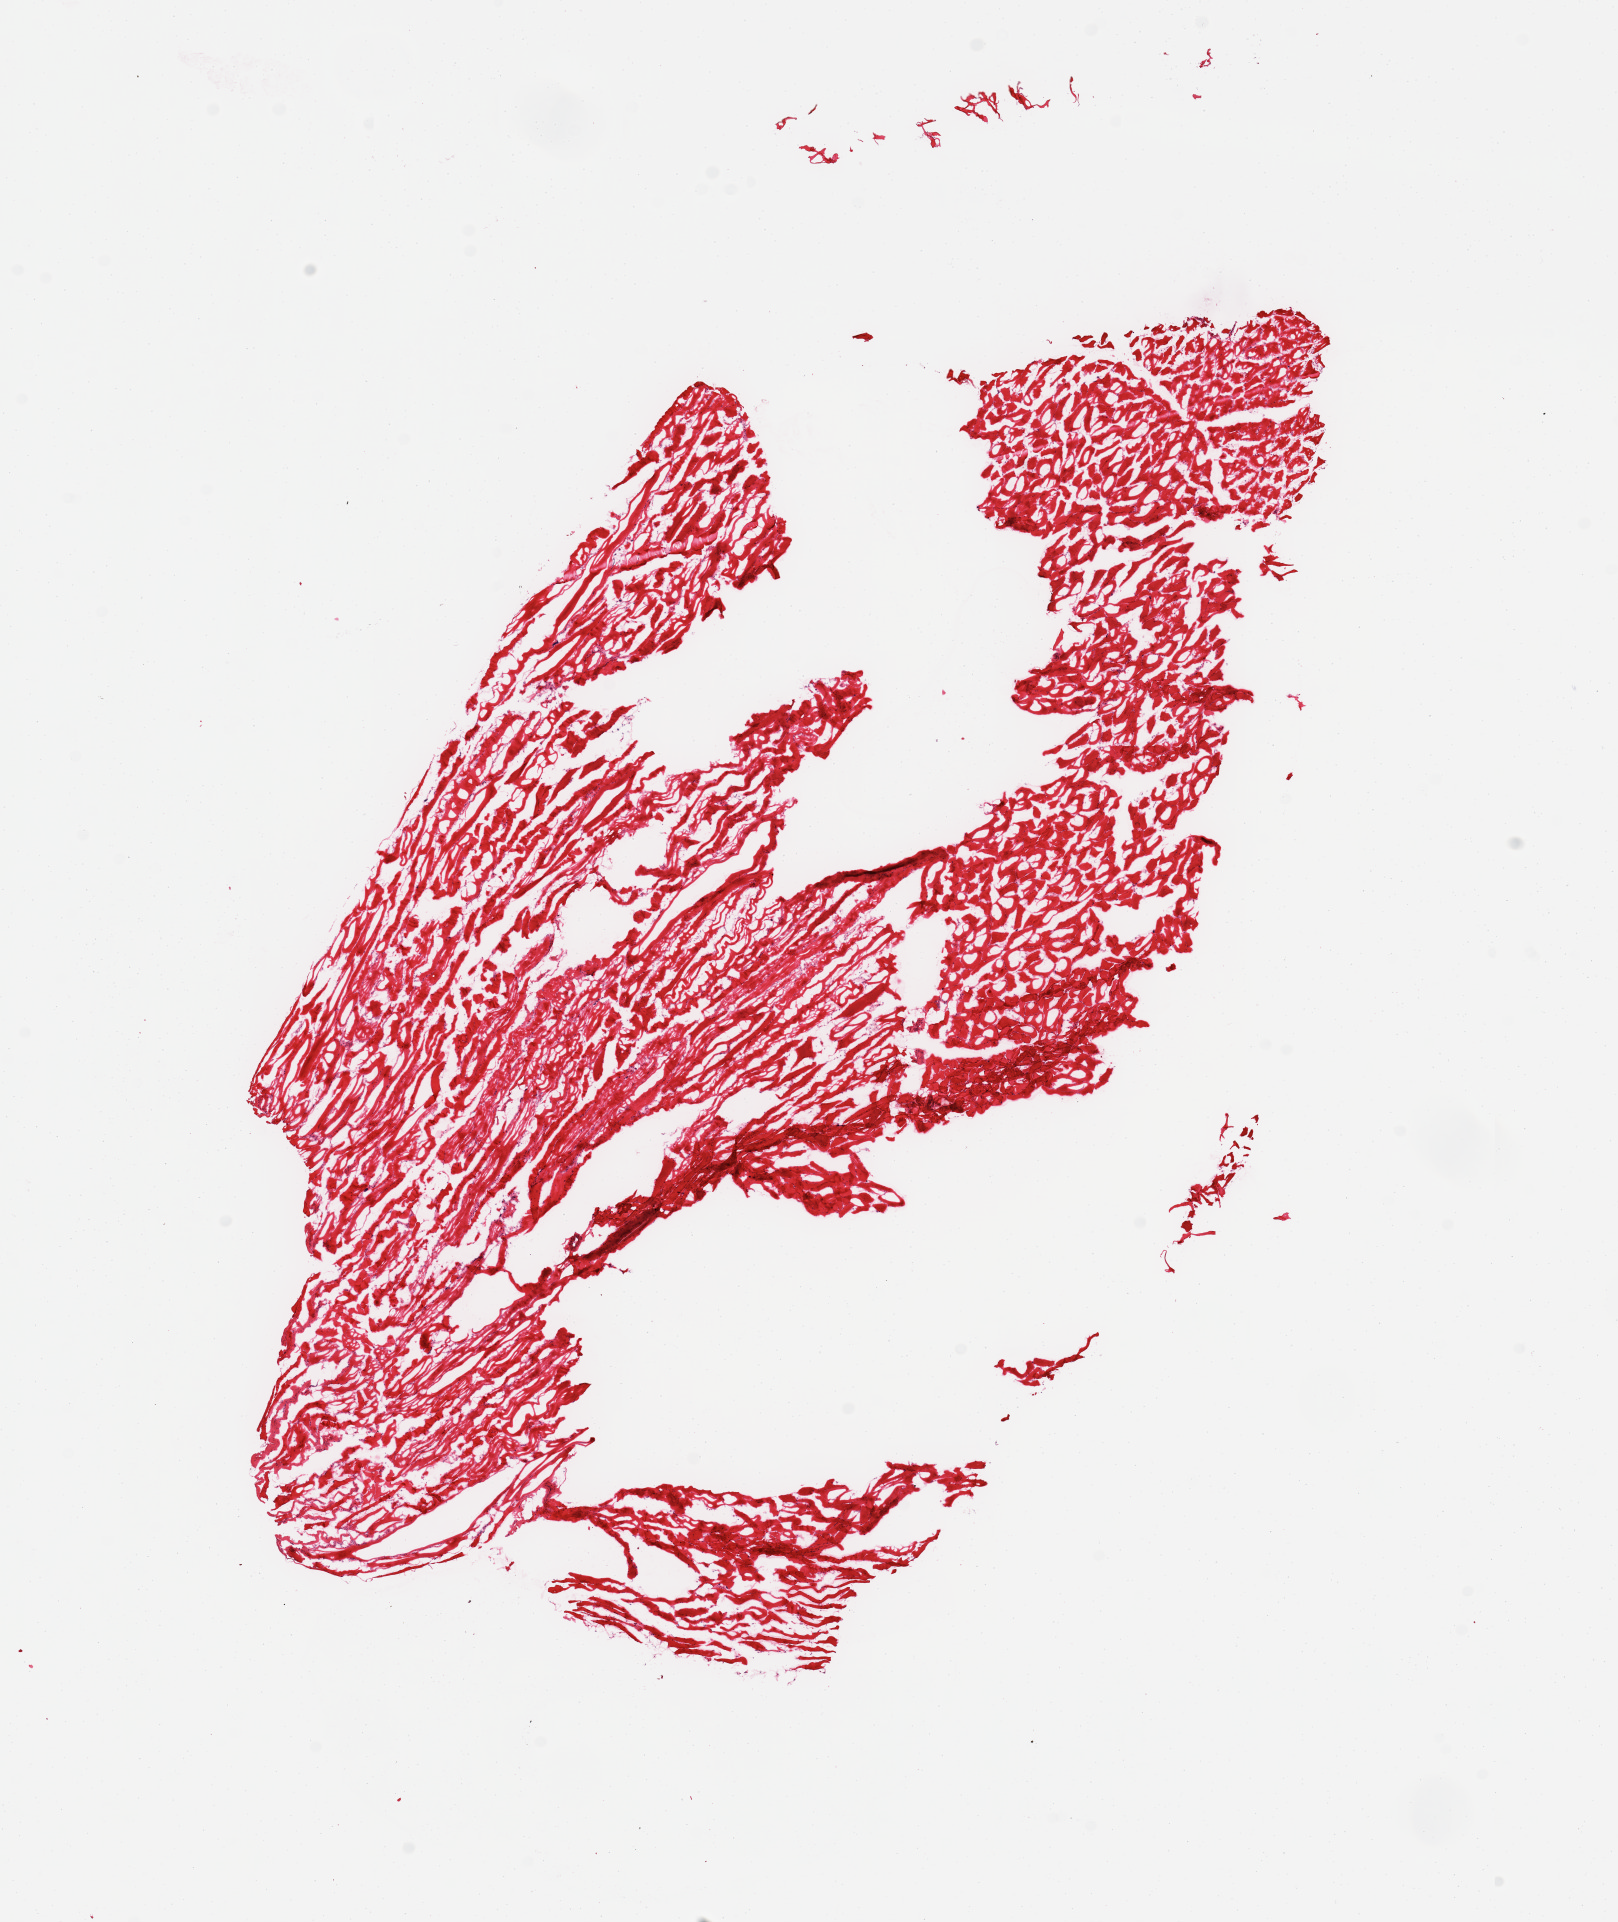
Whole-slide image, haematoxylin and eosin stain — shown as a low-resolution overview of the whole scanned area (about 12.8 x 15.2 mm).
Specimen: frozen section (dry ice); sampled site (target tissue): skeletal muscle; tissue donor sample.